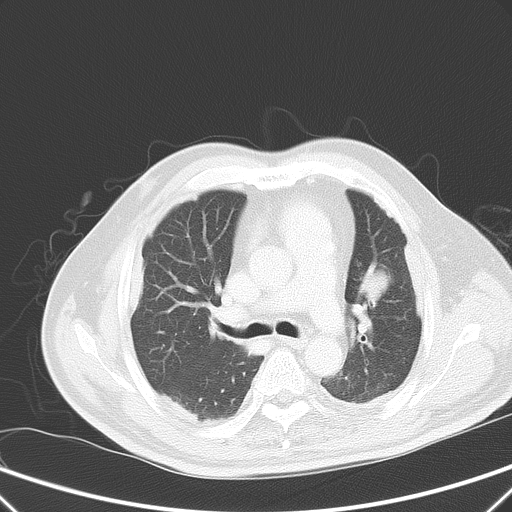
Chest CT, one axial slice. Position 38 of 59 along the scan axis. Intravenous contrast given. Lung window (W 1500 / L -600 HU). 5 mm slice thickness. 512 × 512 image matrix. Male patient, age 66 years. From the clinical record (not read from this slice): clinical TNM (as recorded): T1c N3 M1a.
Structures marked on this image (rectangle marked by the reading radiologist):
- lung tumour (recorded histology: squamous cell carcinoma): bounding box [x1, y1, x2, y2] px = [356, 256, 393, 308]